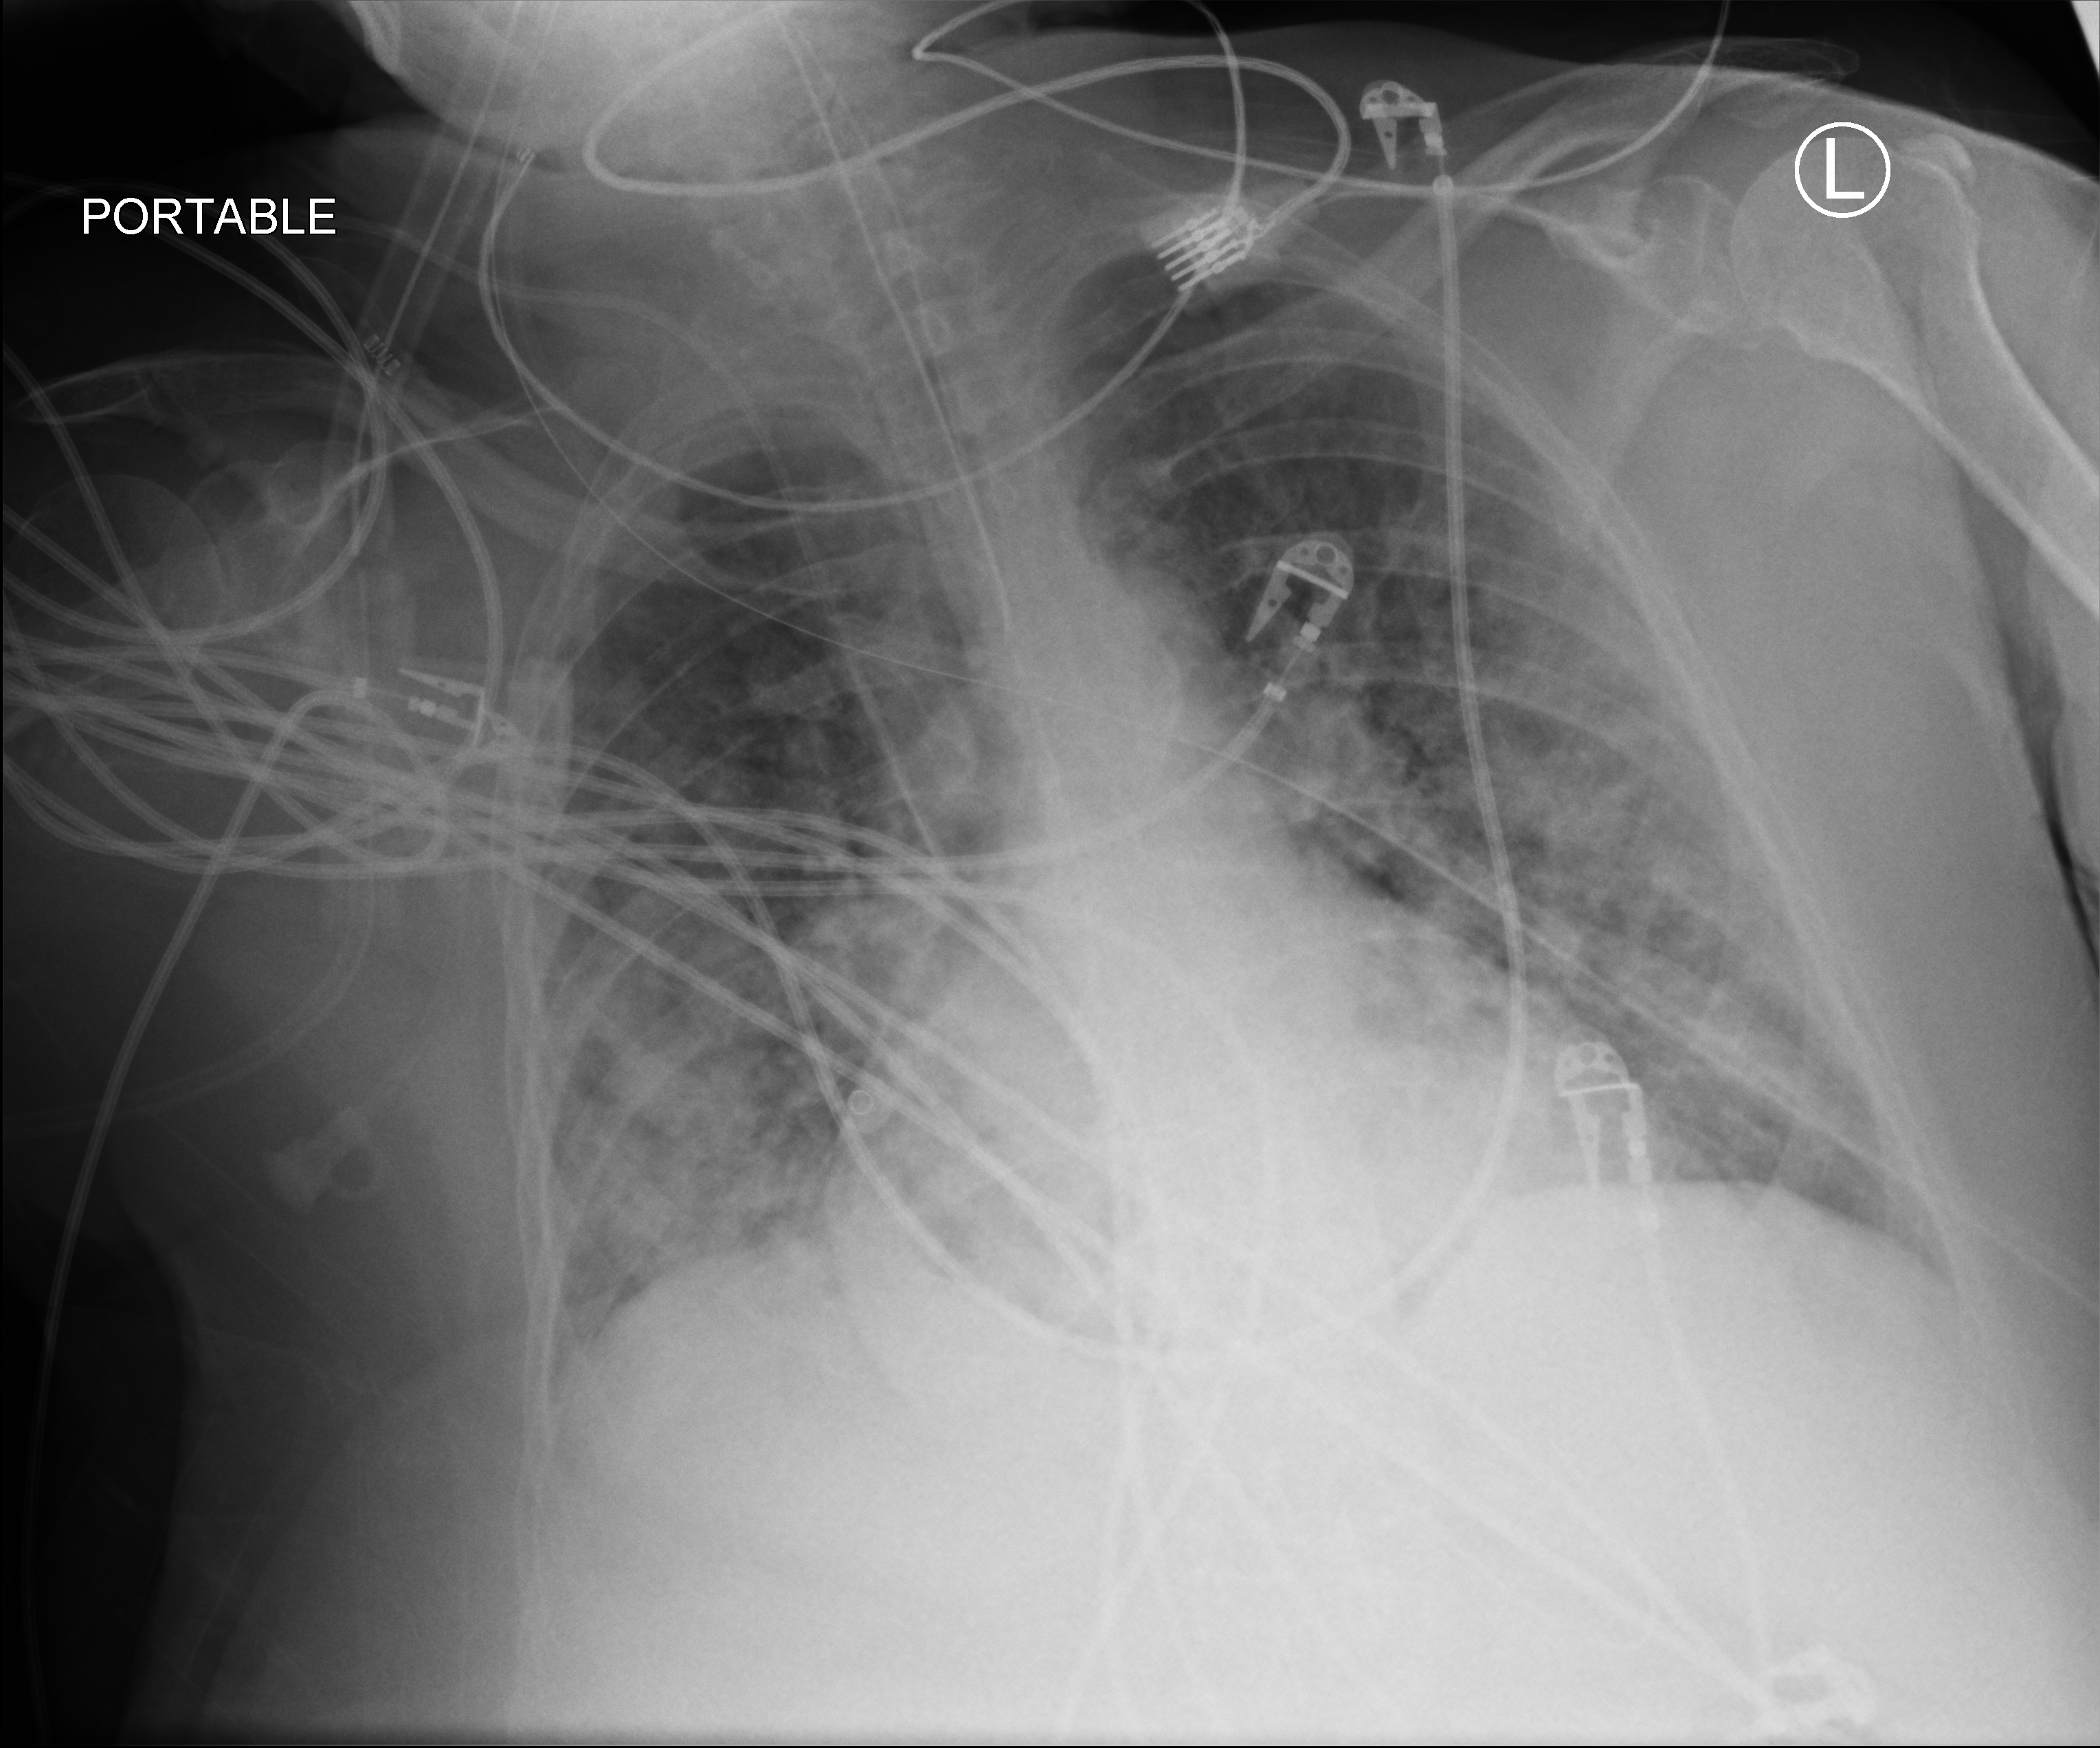
Portable chest radiograph; anteroposterior (AP) projection. Patient hospitalised with COVID-19; female, aged 75–90 years.
From the hospital-stay record, not from the radiograph (when in the stay this image was taken is not recorded): other chronic lung disease (admission record): yes; admitted to intensive care during this hospital stay: yes; COPD (admission record): yes.